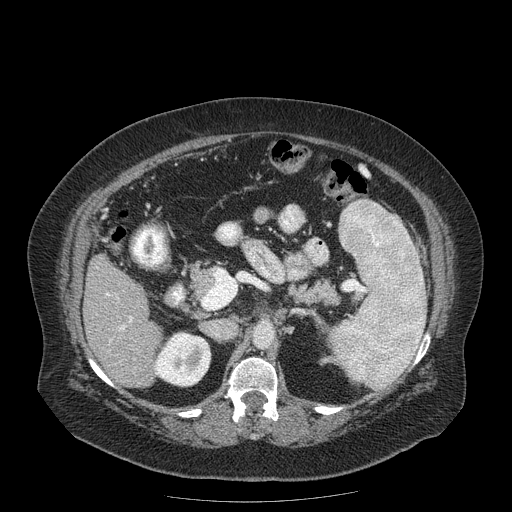
Contrast-enhanced abdominal CT (liver protocol), one axial slice. Slice 79 of 204 in the series (ordered by position). Reconstruction kernel STANDARD. 120 kVp. Soft-tissue window (W 400 / L 40 HU). 512 × 512 image matrix, field of view 440 × 440 mm. Case-level facts recorded for this patient, not image findings: diagnosis: hepatocellular carcinoma (patient treated with transarterial chemoembolisation; whether this scan precedes or follows treatment is not stated here); TNM stage (as recorded): Stage-IIIB.
Annotated regions visible in this slice (semi-automatic segmentation, software-assisted and operator-edited):
- liver parenchyma outside the tumour (the mass and vessels are separate outlines, so this box may not span the whole liver): box from (x=82, y=254) to (x=162, y=388) px
- liver vessels: (x=107, y=293)–(x=133, y=330)